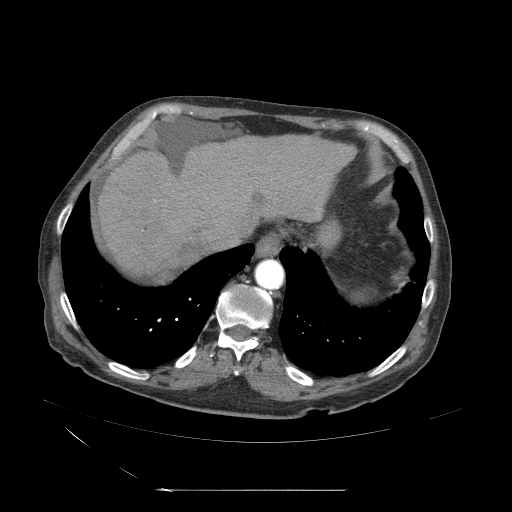
Contrast-enhanced abdominal CT (liver protocol), one axial slice; slice 49 of 71 in the series (ordered by position); soft-tissue window (W 400 / L 40 HU); 2.5 mm slice thickness; 512 × 512 image matrix, field of view 440 × 440 mm. From the clinical record (not read from this slice): diagnosis: hepatocellular carcinoma (patient treated with transarterial chemoembolisation; whether this scan precedes or follows treatment is not stated here); TNM stage (as recorded): Stage-II; Child-Pugh class: A; tumour nodularity: multinodular; tumour size: 1 cm.
Annotated regions visible in this slice (semi-automatic segmentation, software-assisted and operator-edited):
- abdominal aorta: bounding box <254,259,284,289> (left, top, right, bottom; pixels)
- liver parenchyma outside the tumour (the mass and vessels are separate outlines, so this box may not span the whole liver): <99,136,351,280>
- mass: <148,273,177,293>
- liver vessels: <100,195,242,259>